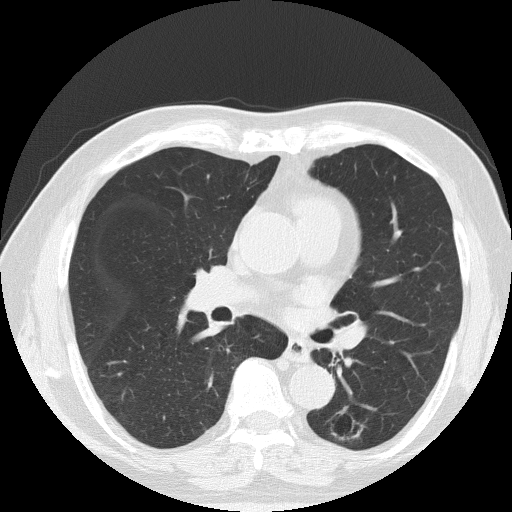
Chest CT (low-dose screening protocol), one axial image, first (baseline) screen, lung window (W 1500 / L -600 HU), slice 76 of 145 in the series. Male, age 71 years at enrolment.
Expert-annotated lung lesion, bounding box [x1, y1, x2, y2] px = [322, 408, 374, 451]. No non-calcified nodule or mass ≥4 mm was recorded by the screening reader at this exam. Lung cancer was diagnosed 340 days after this screen: adenocarcinoma, NOS, left lower lobe, poorly differentiated (G3), stage IA (AJCC 6th edition), 28 mm at pathology.